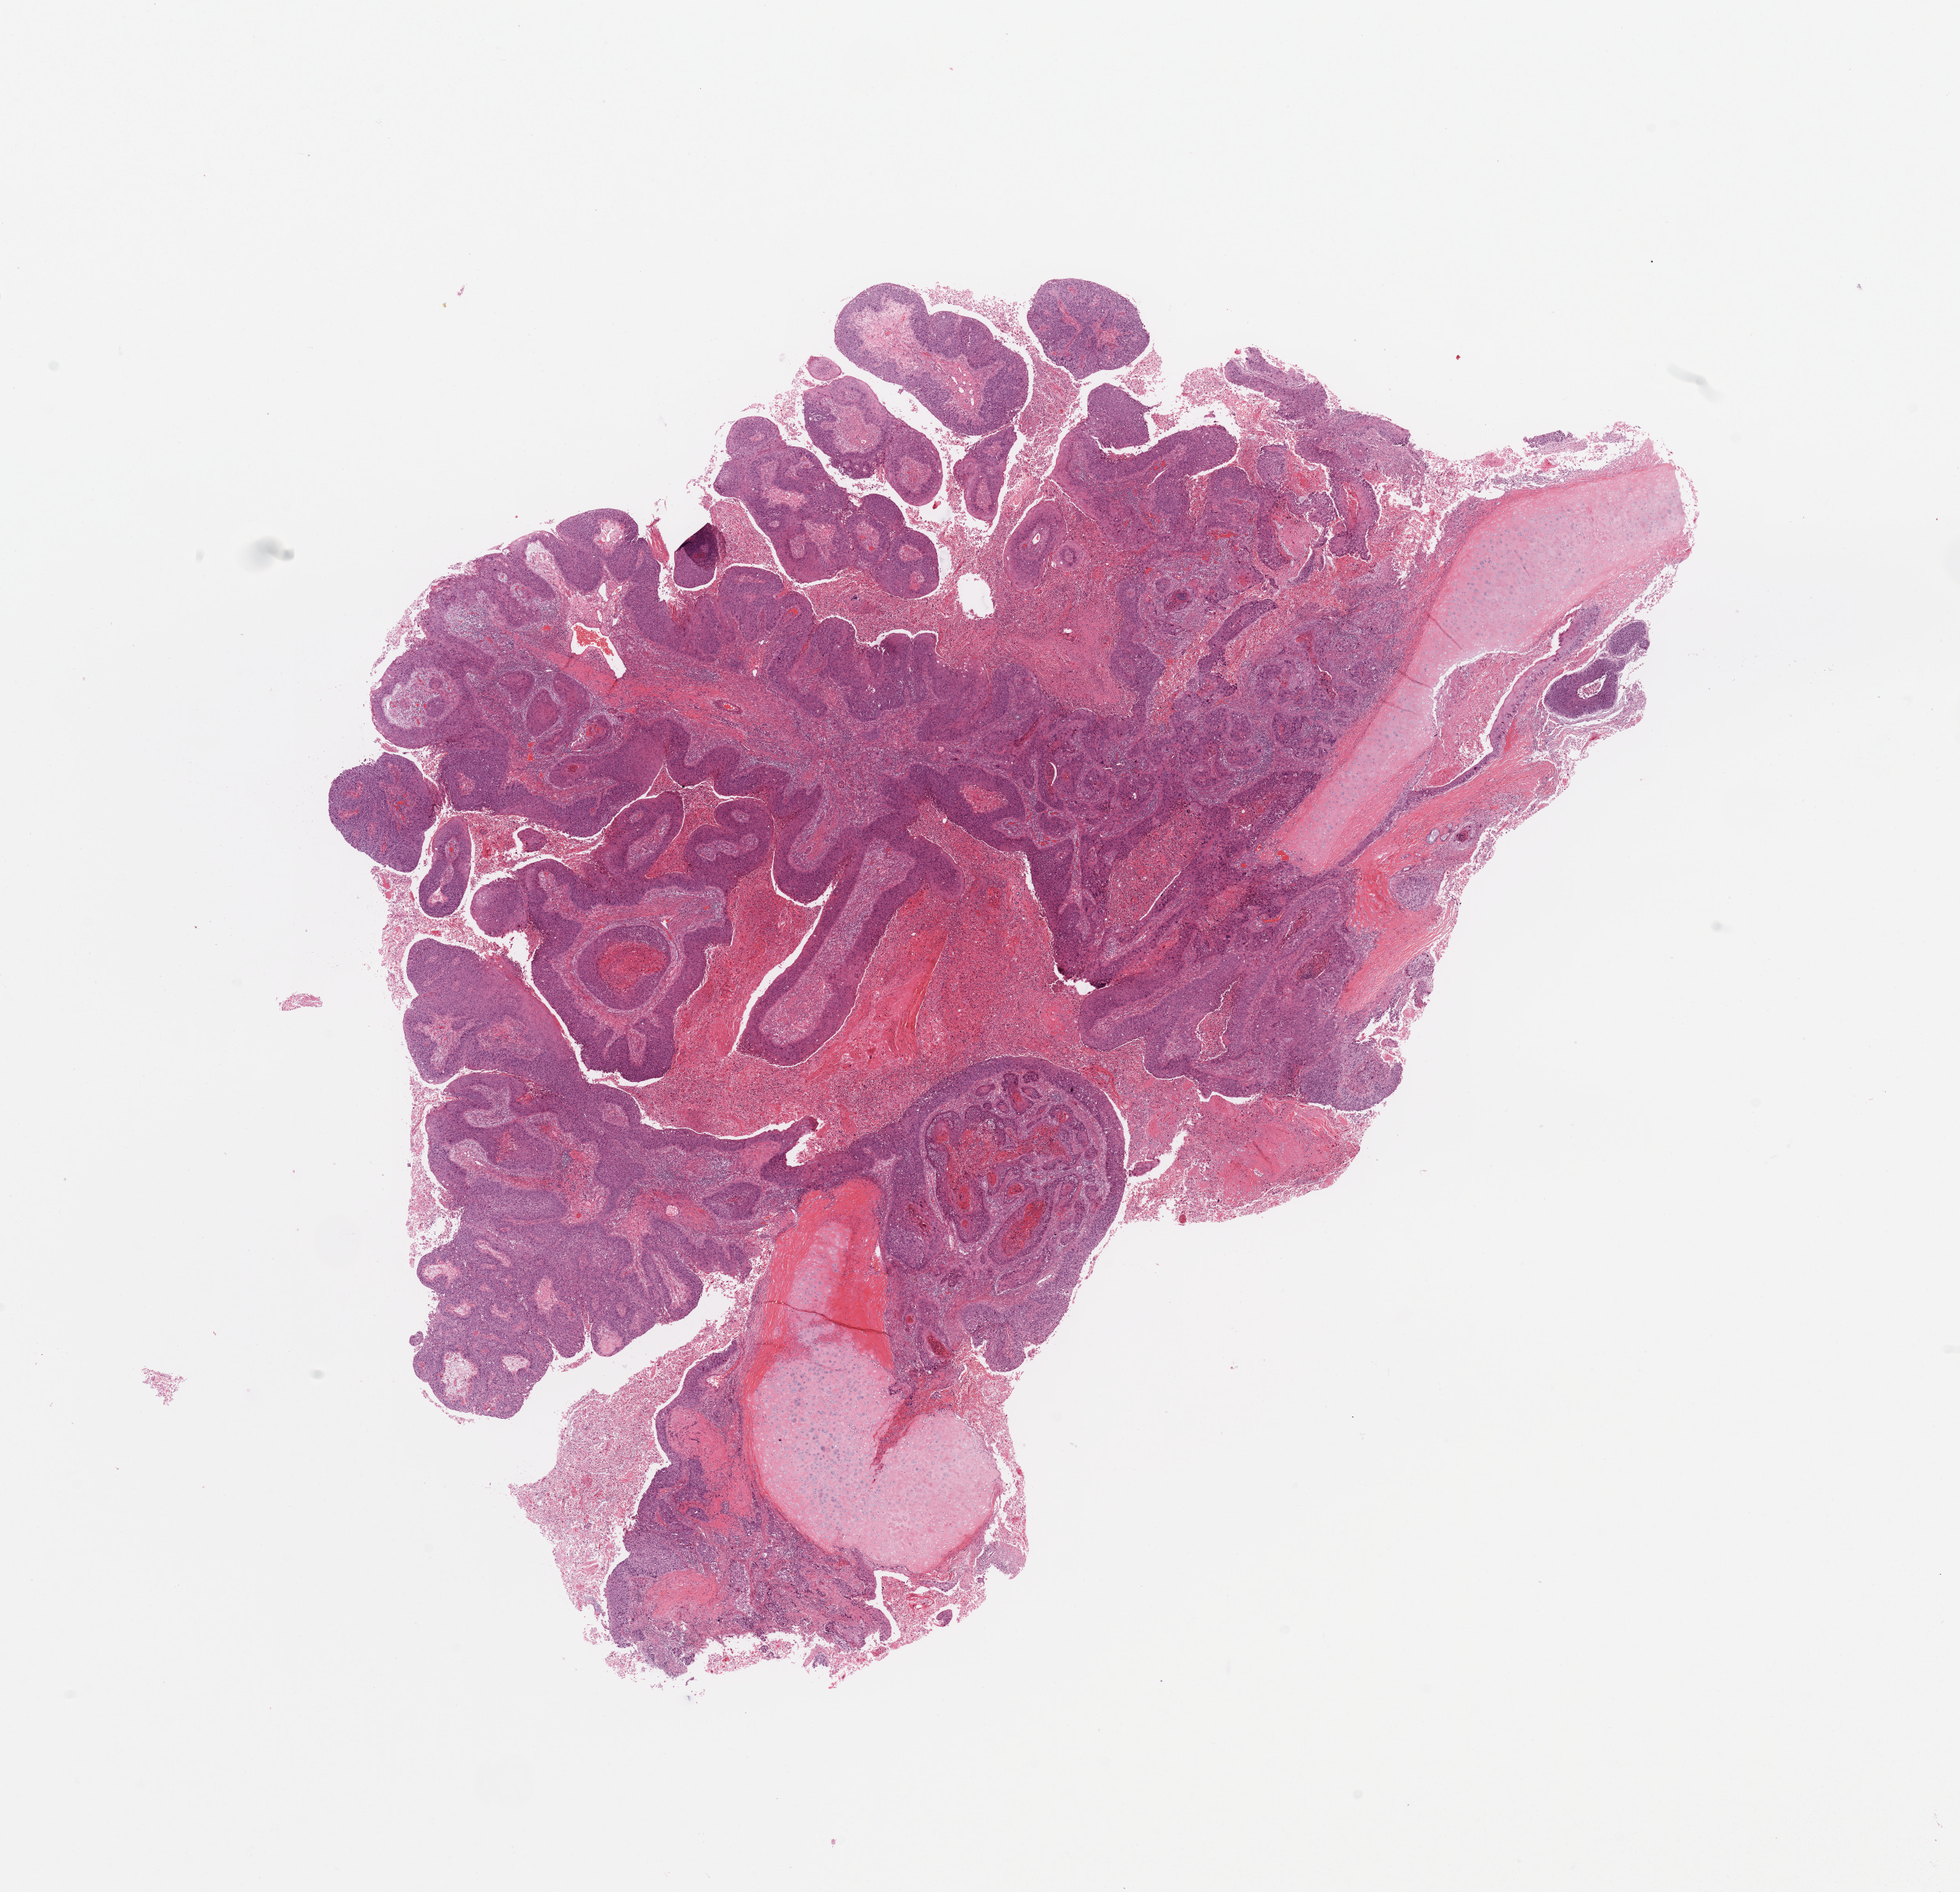
H&E whole-slide image — whole scanned area (about 19.7 x 19.0 mm) shown as a low-resolution overview. Tumour tissue sample, sampled site: lung. Patient: male, age 67 years. Histologic grade: G2 (moderately differentiated). Slide review estimates, as recorded: tumour nuclei 60%, necrosis 20%.
AJCC pathologic stage: IIA. Diagnosis: Squamous cell carcinoma, NOS.